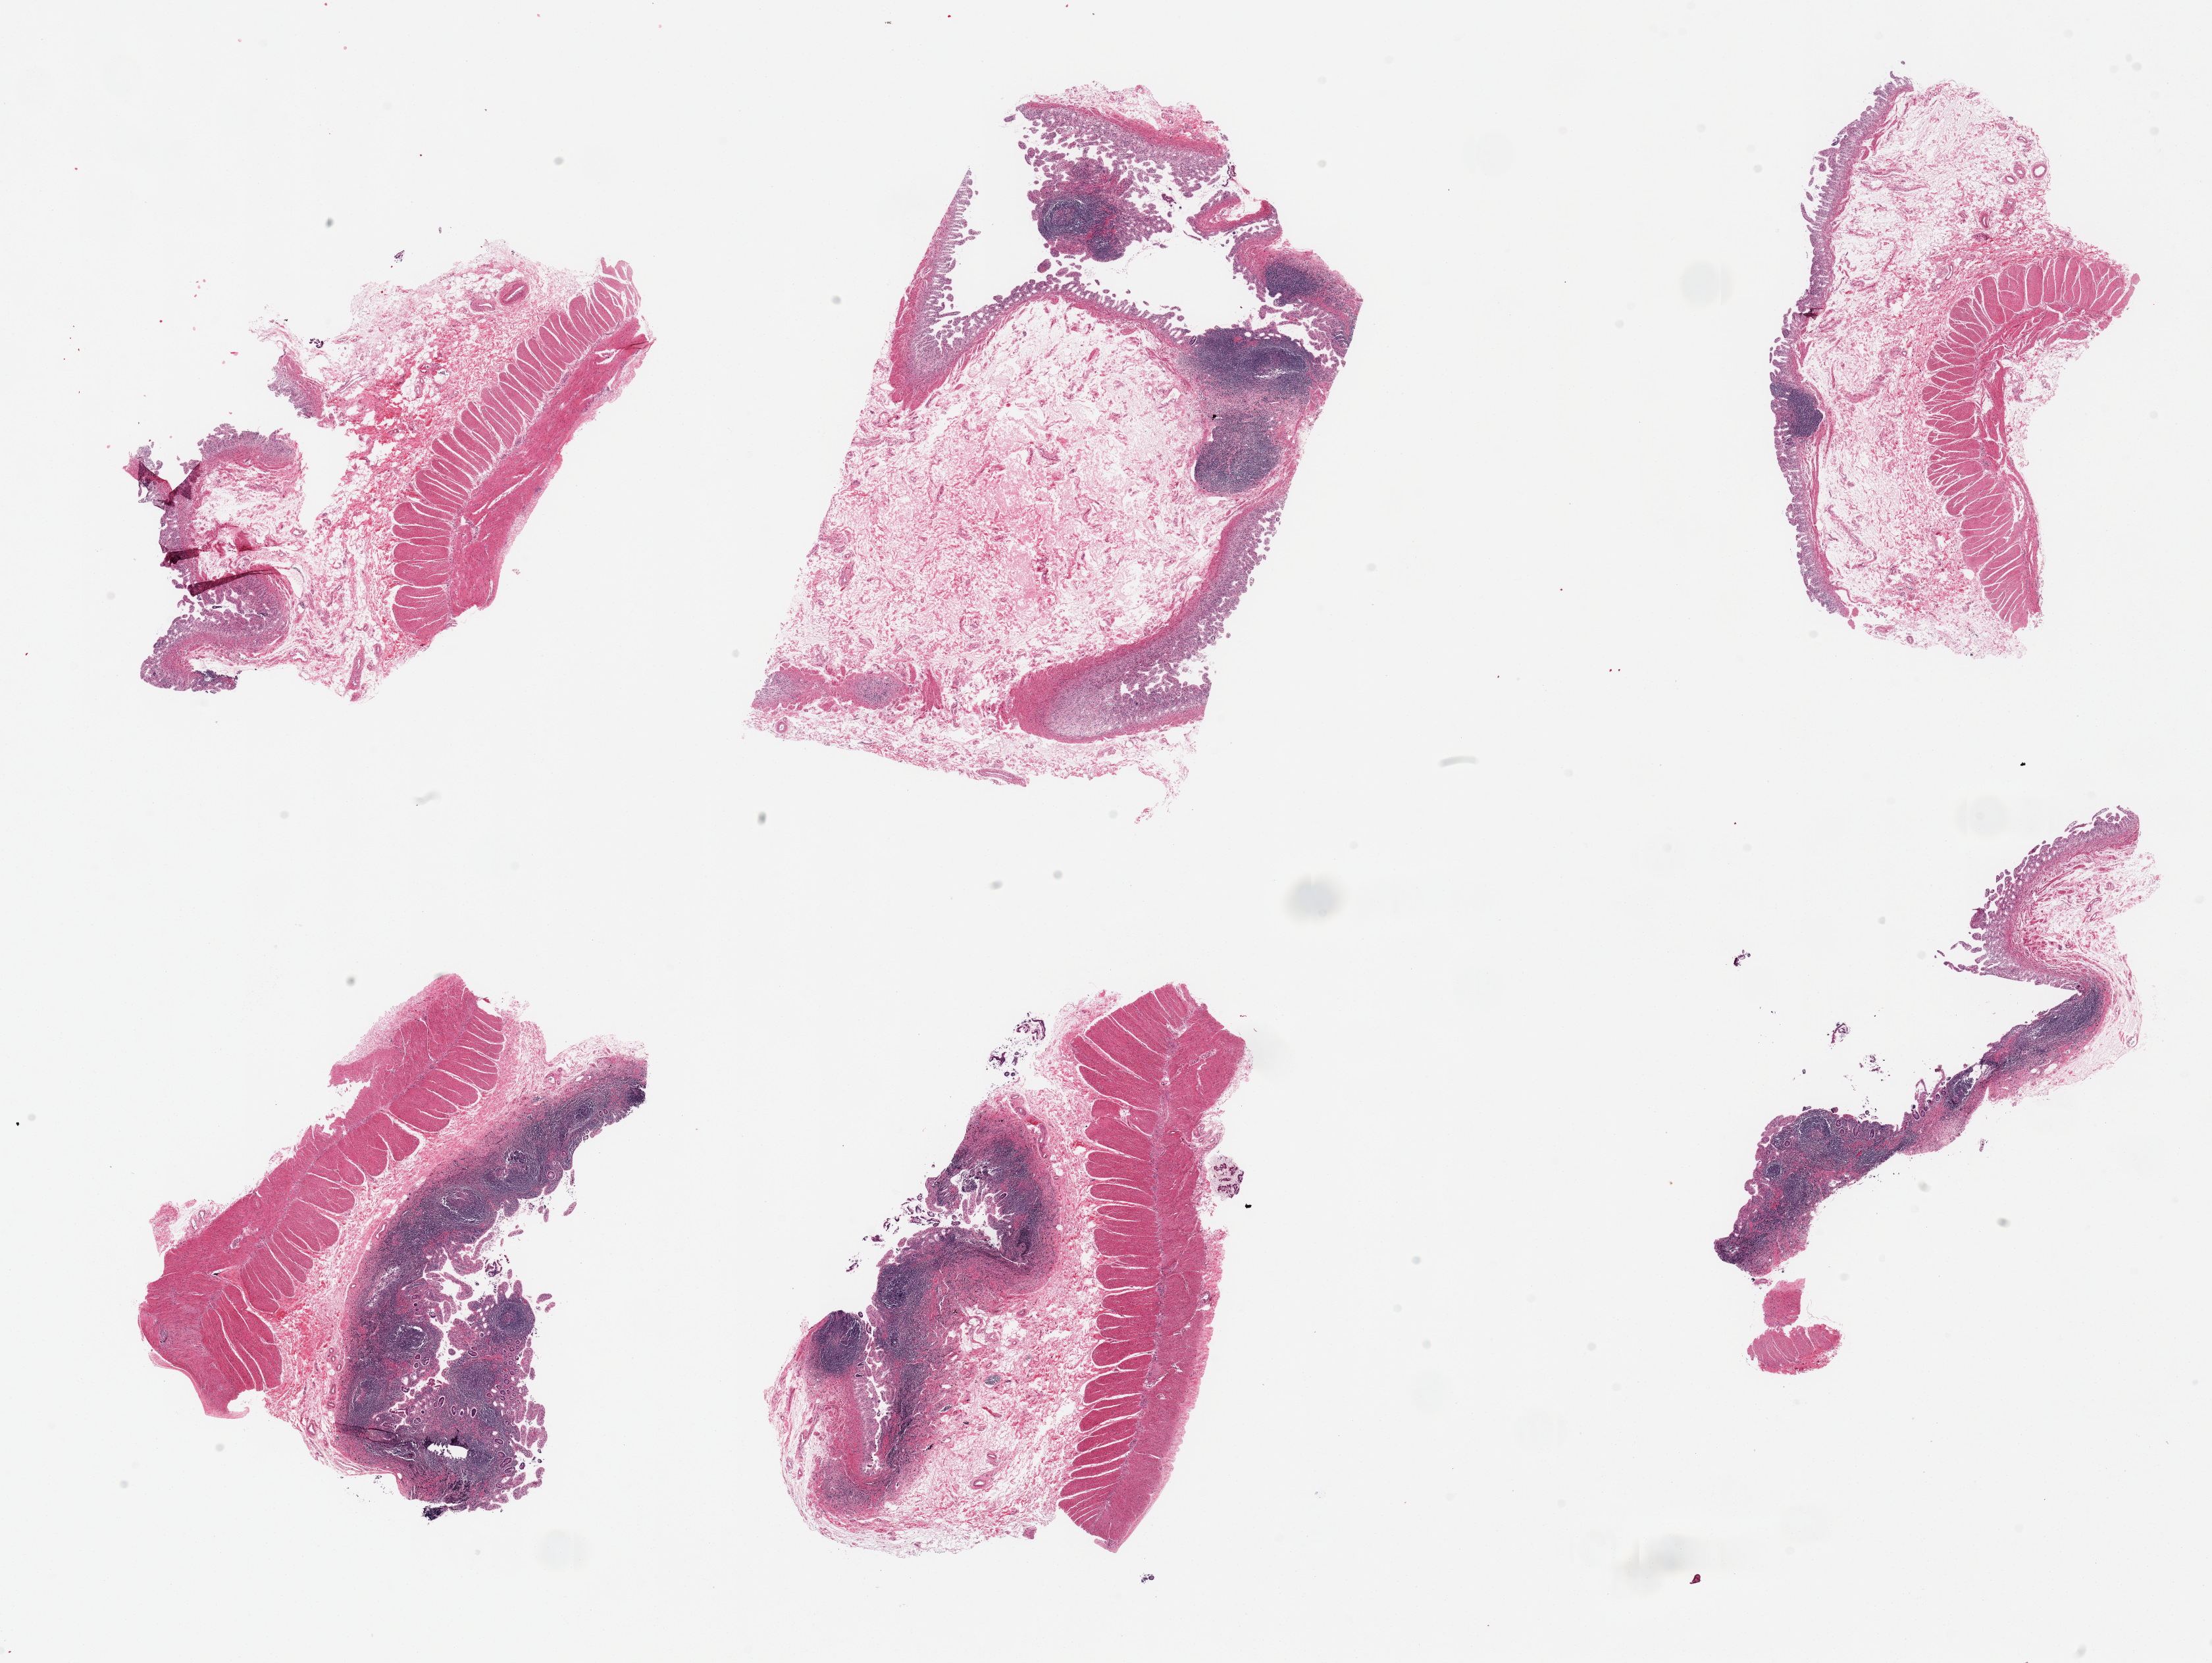
Hematoxylin and eosin (H&E) whole-slide image, a low-resolution overview of the entire scanned area, about 26.6 x 20.0 mm (slide scanned at 20x). Donor: female.
Specimen: PAXgene-fixed paraffin-embedded (PFPE) section; sampled site (target tissue): ileum; donor tissue sample.